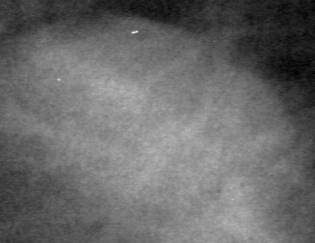
Cropped region of a digitized screen-film mammogram centred on a radiologist-marked abnormality, right breast, MLO view.
- Marked abnormality: mass, shape oval, margins obscured; BI-RADS assessment category 4; pathology (as recorded): benign.